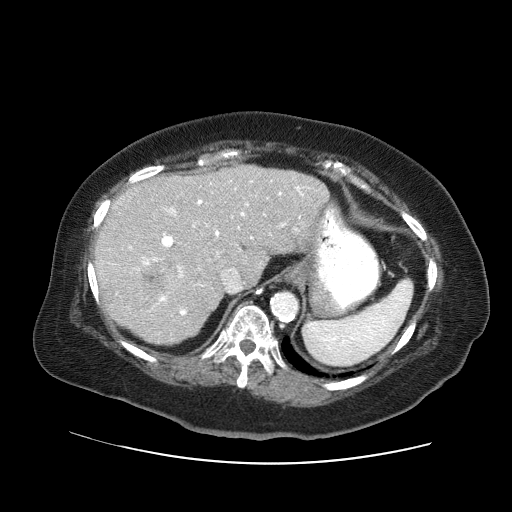
Contrast-enhanced abdominal CT (liver protocol), one axial slice; slice 41 of 71 in the series (ordered by position); reconstruction kernel STANDARD; 120 kVp; soft-tissue window (W 400 / L 40 HU); 2.5 mm slice thickness; 512 × 512 image matrix, field of view 400 × 400 mm. From the clinical record (not read from this slice): diagnosis: hepatocellular carcinoma (patient treated with transarterial chemoembolisation; whether this scan precedes or follows treatment is not stated here); TNM stage (as recorded): Stage-II; Child-Pugh class: A; tumour differentiation: poorly differentiated; tumour nodularity: multinodular.
Outlined on this slice (semi-automatically segmented with operator editing):
- liver parenchyma outside the tumour (the mass and vessels are separate outlines, so this box may not span the whole liver): bounding box [x1, y1, x2, y2] px = [94, 164, 328, 344]
- mass: [138, 263, 181, 293]
- liver vessels: [129, 180, 305, 315]